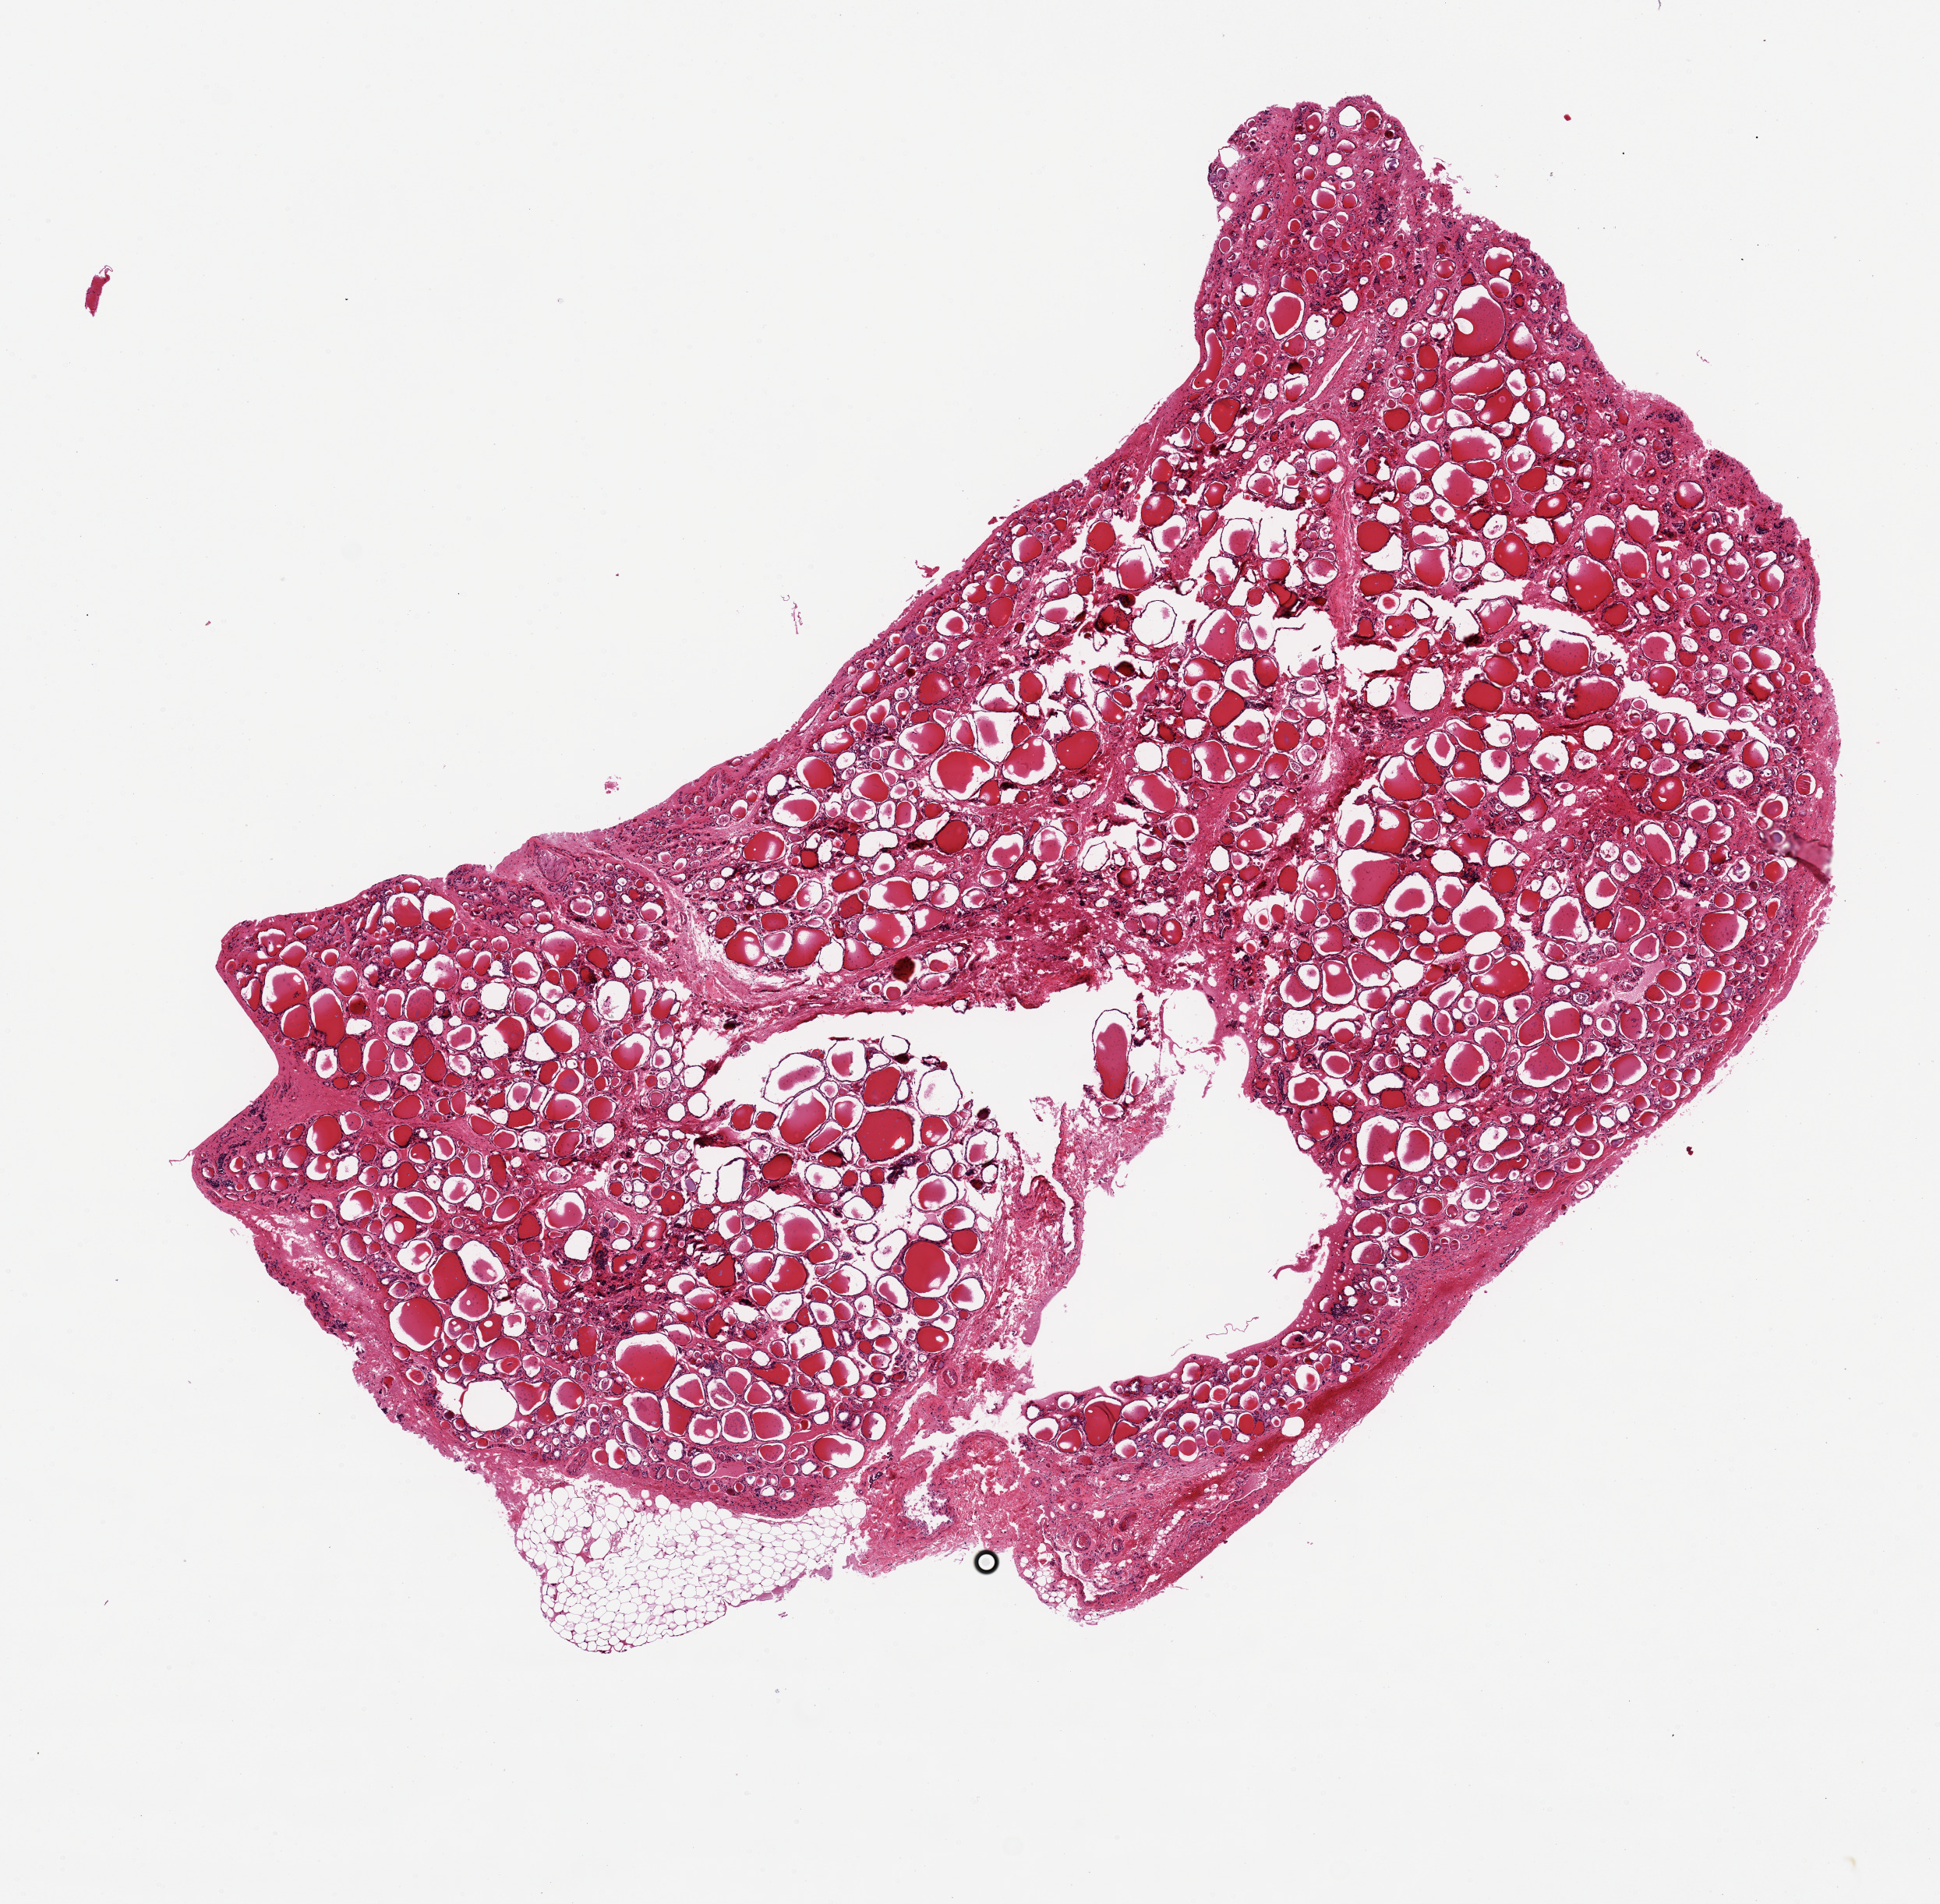
Whole-slide image, hematoxylin and eosin (H&E) stain, brightfield — shown as a low-resolution overview of the whole scanned area (about 9.8 x 9.7 mm); PAXgene-fixed paraffin-embedded (PFPE) section; sampled site (target tissue): thyroid; tissue donor sample. Female donor.
• pathologist's review note for this sample: 8x4 mm